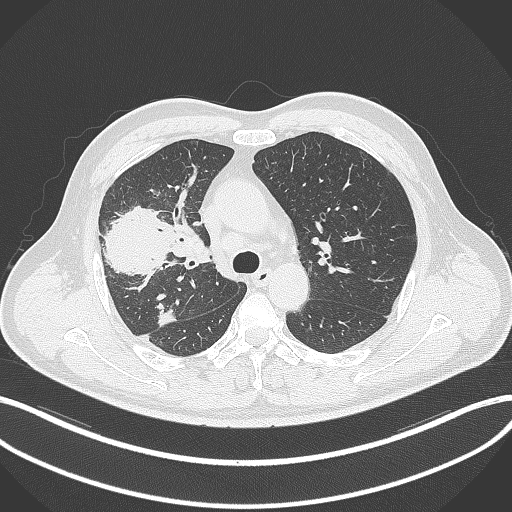
Chest CT, one axial slice; position 226 of 348 along the scan axis; 120 kVp; lung window (W 1500 / L -600 HU); 1 mm slice thickness; 512 × 512 image matrix, field of view 400 × 400 mm. Patient: male, 55 years. From the clinical record (not read from this slice): clinical TNM (as recorded): T3 N2 M1.
Outlined on this slice (rectangle marked by the reading radiologist):
- lung tumour (recorded histology: adenocarcinoma): bounding box <100,201,173,280> (left, top, right, bottom; pixels)